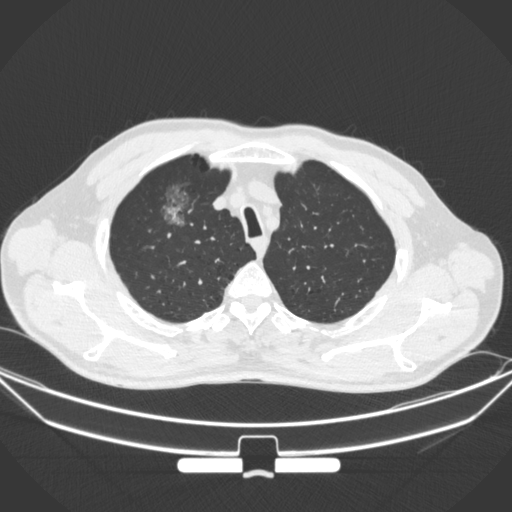
Chest CT, one axial slice; position 286 of 355 along the scan axis; lung window (W 1500 / L -600 HU); 512 × 512 image matrix, field of view 399 × 399 mm. Male patient, age 67 years. Case-level facts recorded for this patient, not image findings: clinical TNM (as recorded): T1c N0 M0; histopathological grade: G2.
Outlined on this slice (bounding box drawn by a radiologist):
- lung tumour (recorded histology: adenocarcinoma): bounding box [x1, y1, x2, y2] px = [150, 174, 202, 237]